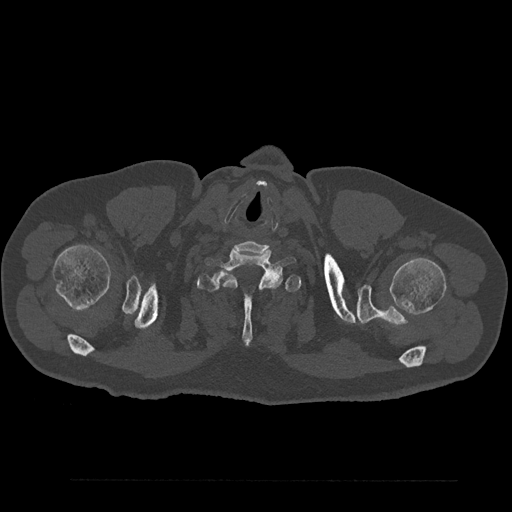
CT including the spine, one axial slice. 120 kVp. Bone window (W 1800 / L 400 HU). 512 × 512 image matrix, field of view 430 × 430 mm. Patient: male, 61 years. Case-level facts recorded for this patient, not image findings: primary cancer: prostate.
Outlined on this slice (semi-automatic segmentation, software-assisted and operator-edited):
- T1 vertebra: bounding box (x1, y1, x2, y2) in pixels: (197, 257, 302, 345)